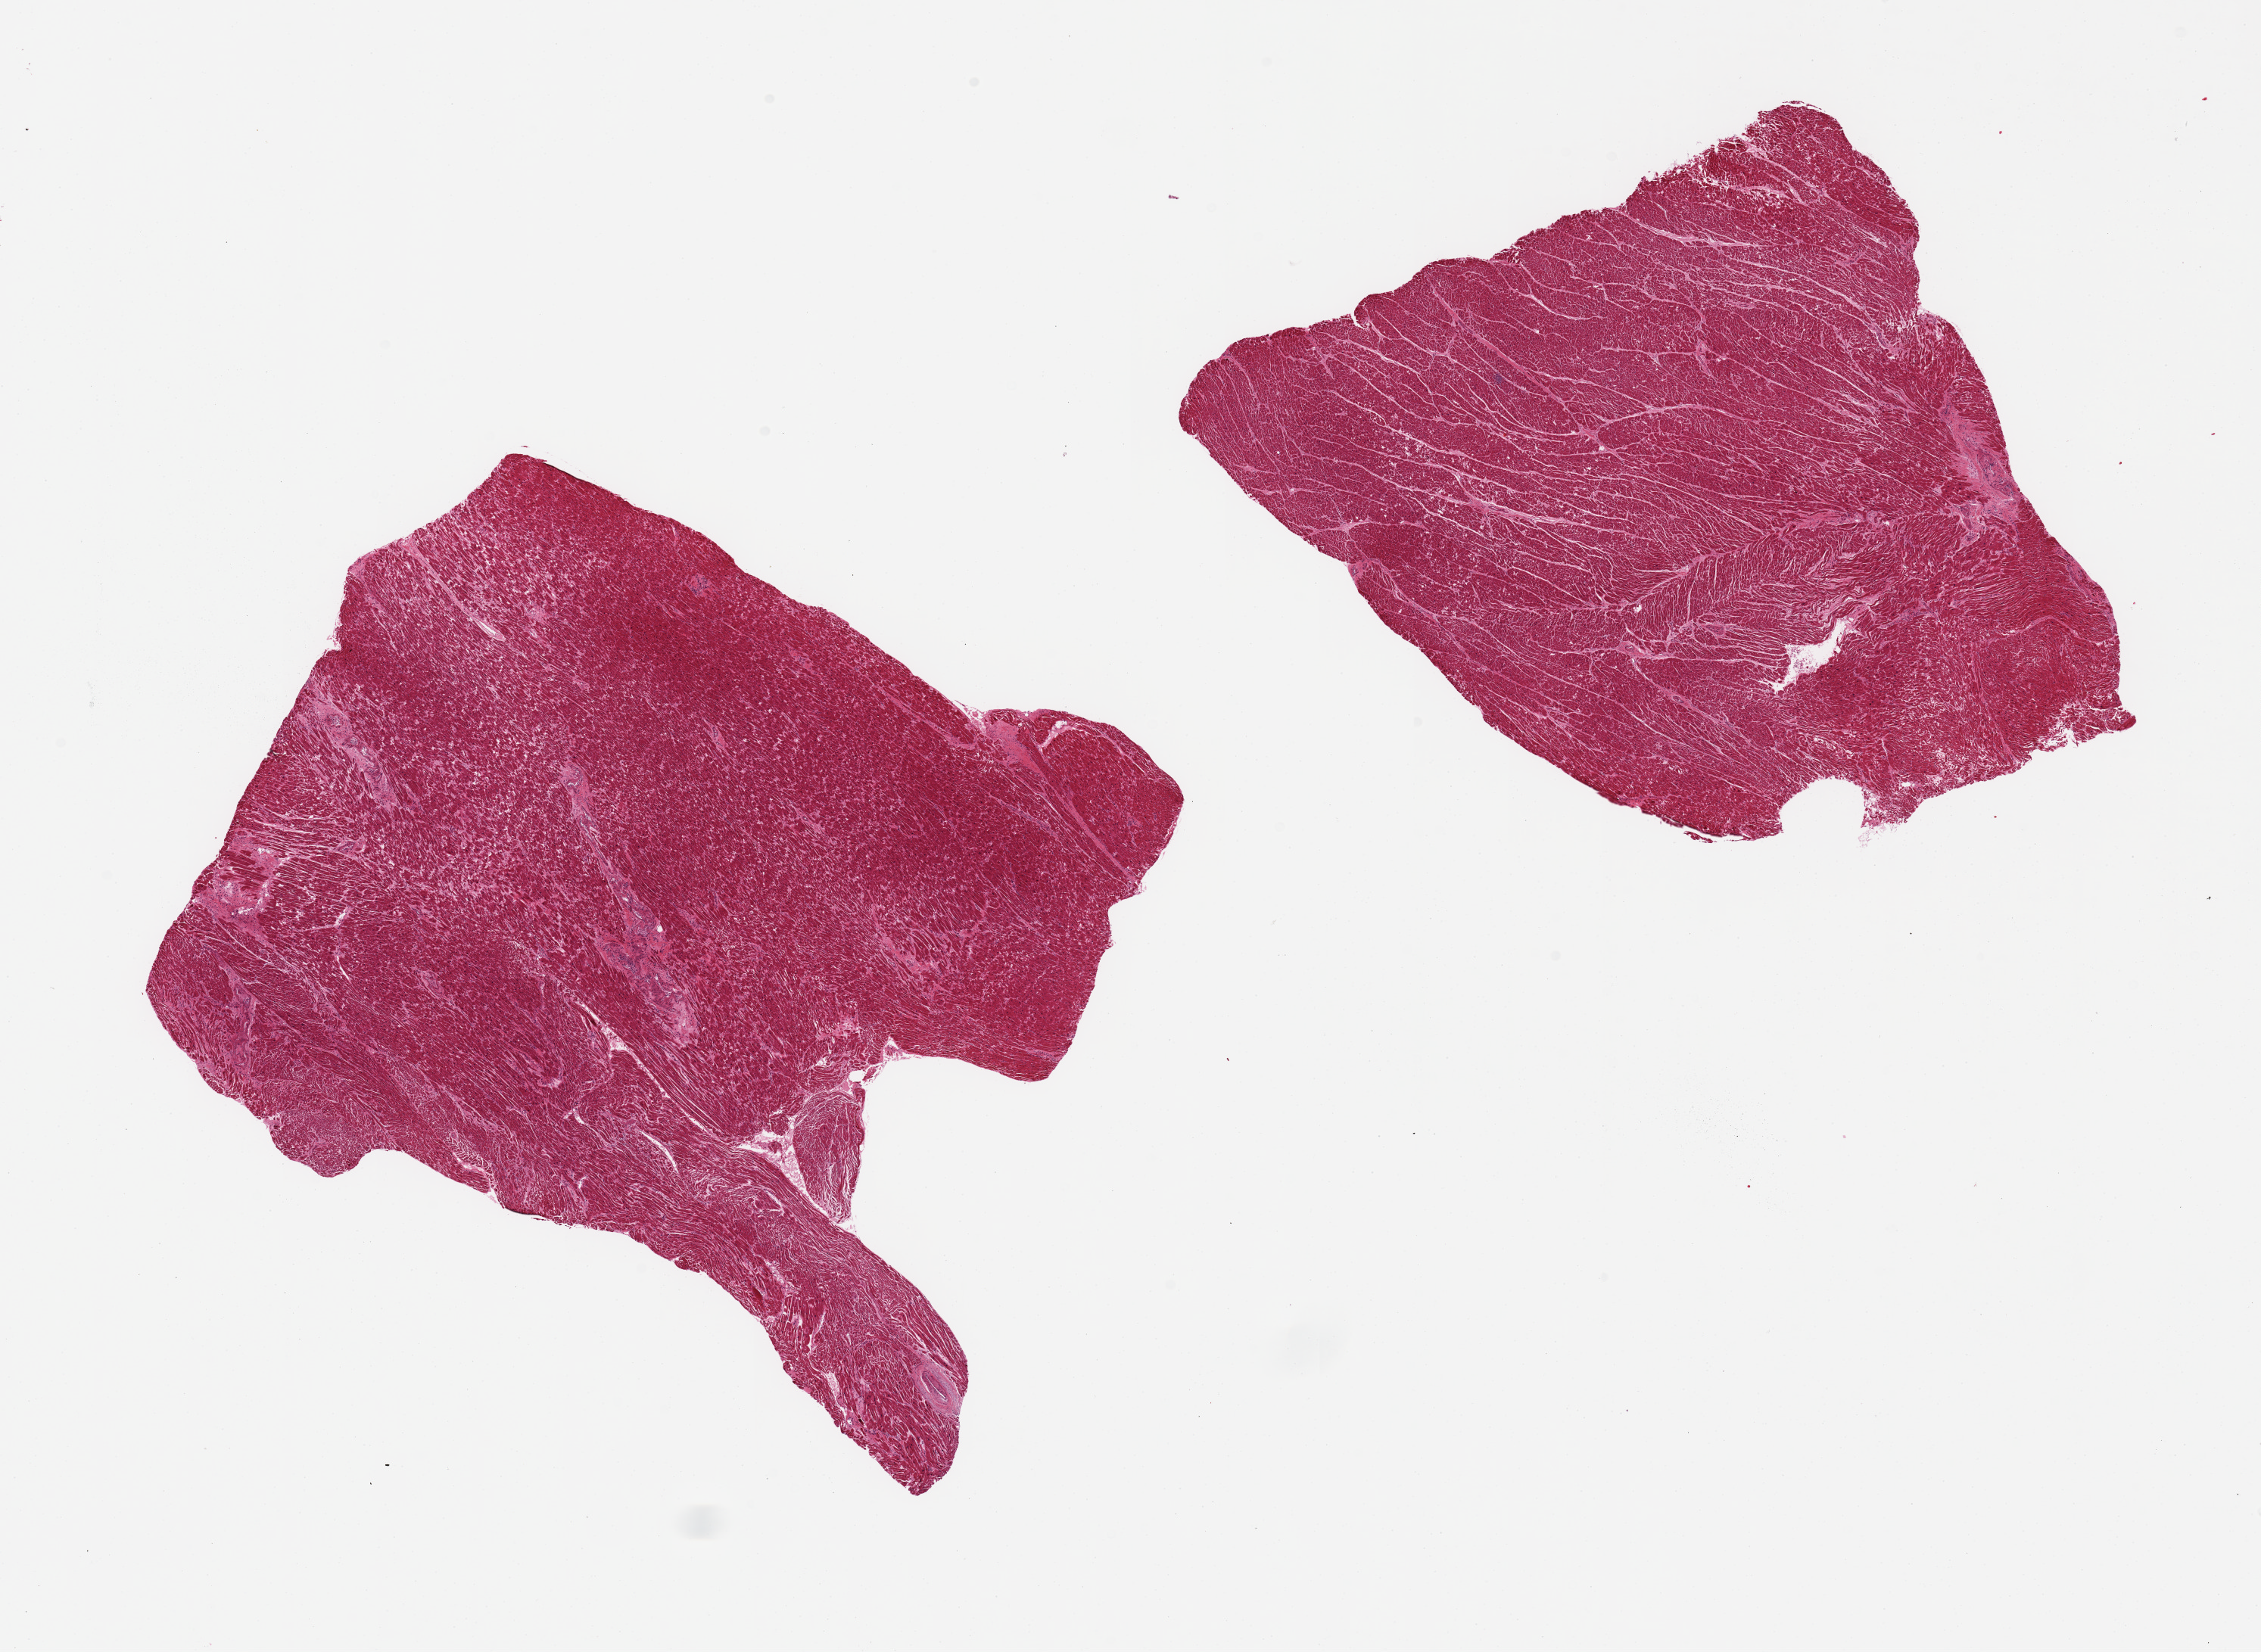
Digitized haematoxylin and eosin-stained section, brightfield, shown as a low-resolution overview of the whole scanned area (about 23.6 x 17.3 mm, acquisition: 20x scan). PAXgene-fixed paraffin-embedded (PFPE) section. Sampled site (target tissue): heart. Donor tissue sample. Donor sex: female.
Review note (as recorded): 2 pieces chronic ischemic changes, interstitial fibrosis, microinfarct.